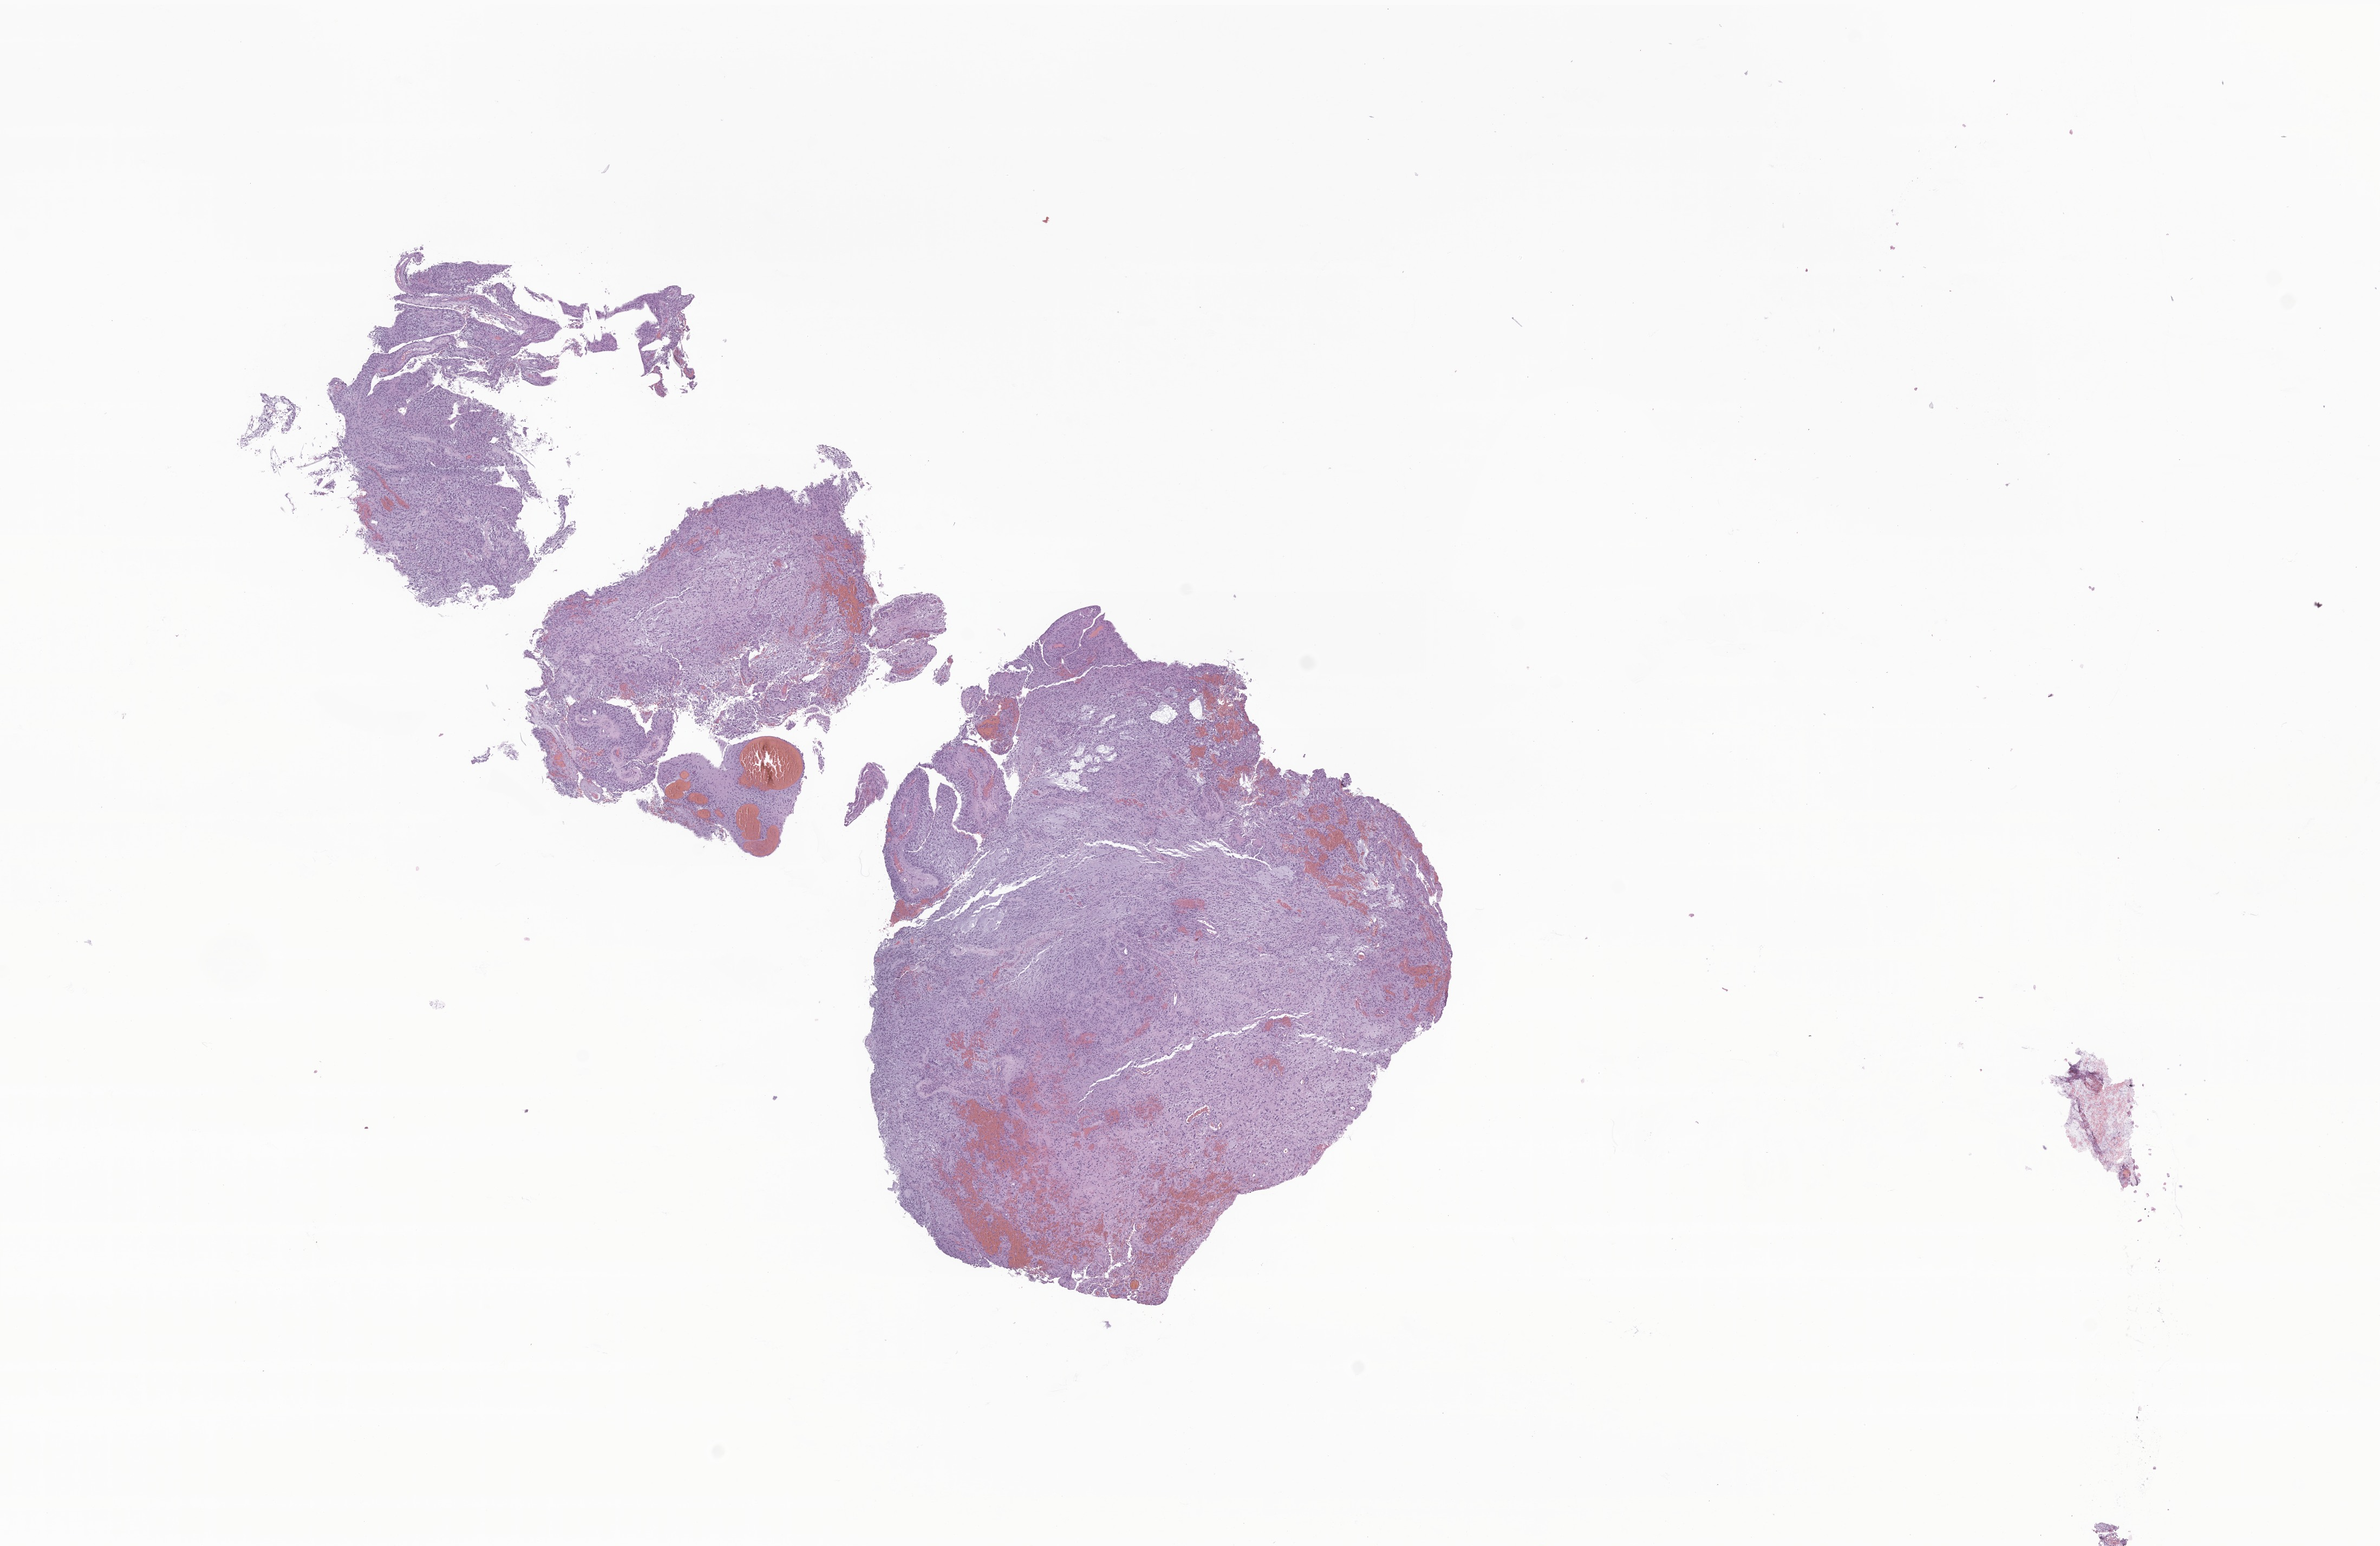
Whole-slide image, hematoxylin and eosin (H&E) stain of tumor tissue from the brain, shown as a low-resolution overview of the whole scanned area (about 18.5 x 12.0 mm); formalin-fixed, paraffin-embedded (FFPE) tissue. Male patient, age 169 months.
* diagnosis (ICD-O-3 morphology term): Glioma, malignant